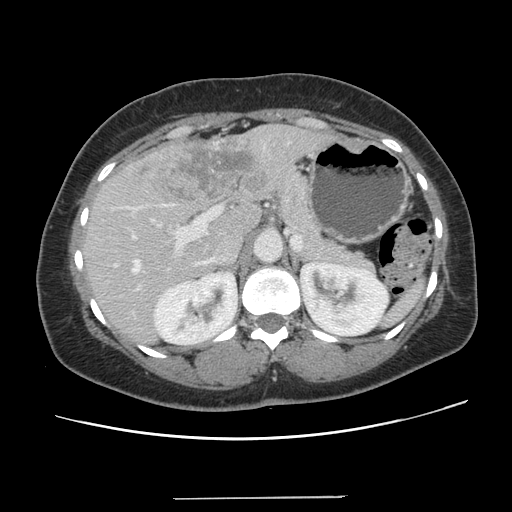
Contrast-enhanced abdominal CT, one axial slice. Slice 80 of 141 in the series (ordered by position). Intravenous contrast given. Soft-tissue window (W 400 / L 40 HU). 512 × 512 image matrix, field of view 366 × 366 mm. Female patient, age 53 years. From the clinical record (not read from this slice): diagnosis: colorectal cancer liver metastases, imaged before liver resection.
Structures marked on this image (outlined manually by an expert reader):
- hepatic veins: bounding box (x1, y1, x2, y2) in pixels: (132, 259, 139, 272)
- liver: (84, 125, 332, 344)
- planned liver remnant (the part of the liver to remain after resection): (85, 205, 261, 344)
- portal vein (with intrahepatic branches): (132, 204, 219, 291)
- liver metastasis: (134, 137, 269, 203)